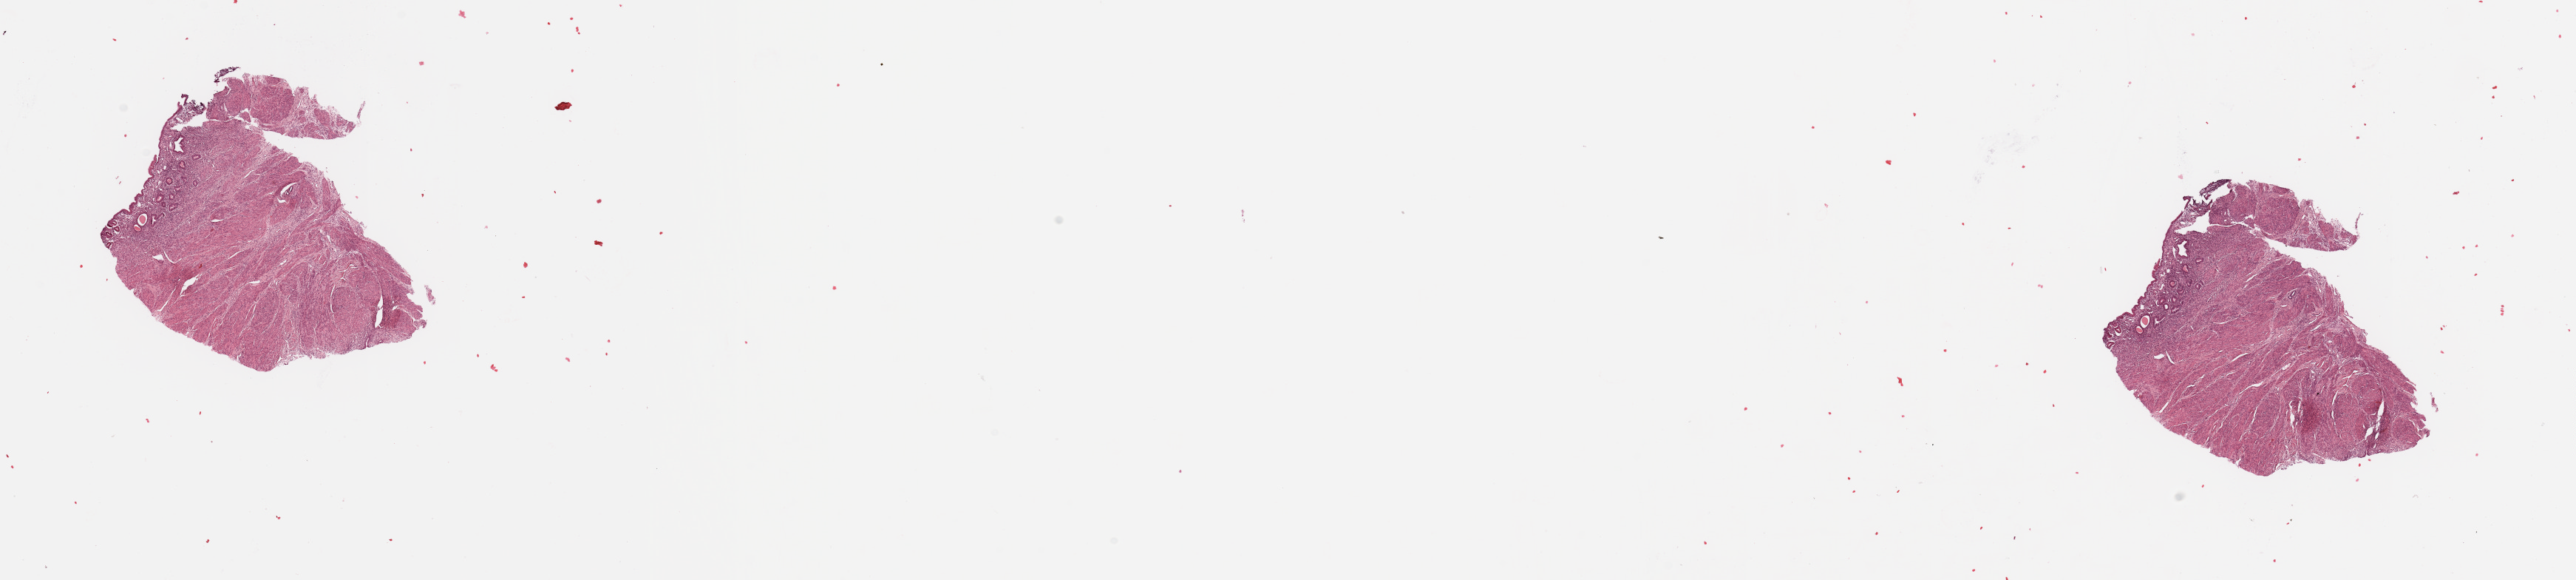
Hematoxylin and eosin (H&E) stained whole-slide image — shown as a low-resolution overview of the whole scanned area (about 27.6 x 6.2 mm, from a 20x scan), normal (non-tumour) tissue sample, sampled site: uterus. Patient: female, age 73 years.
This section: normal (non-tumour) tissue from the same patient. Patient diagnosis: Endometrioid adenocarcinoma, NOS.